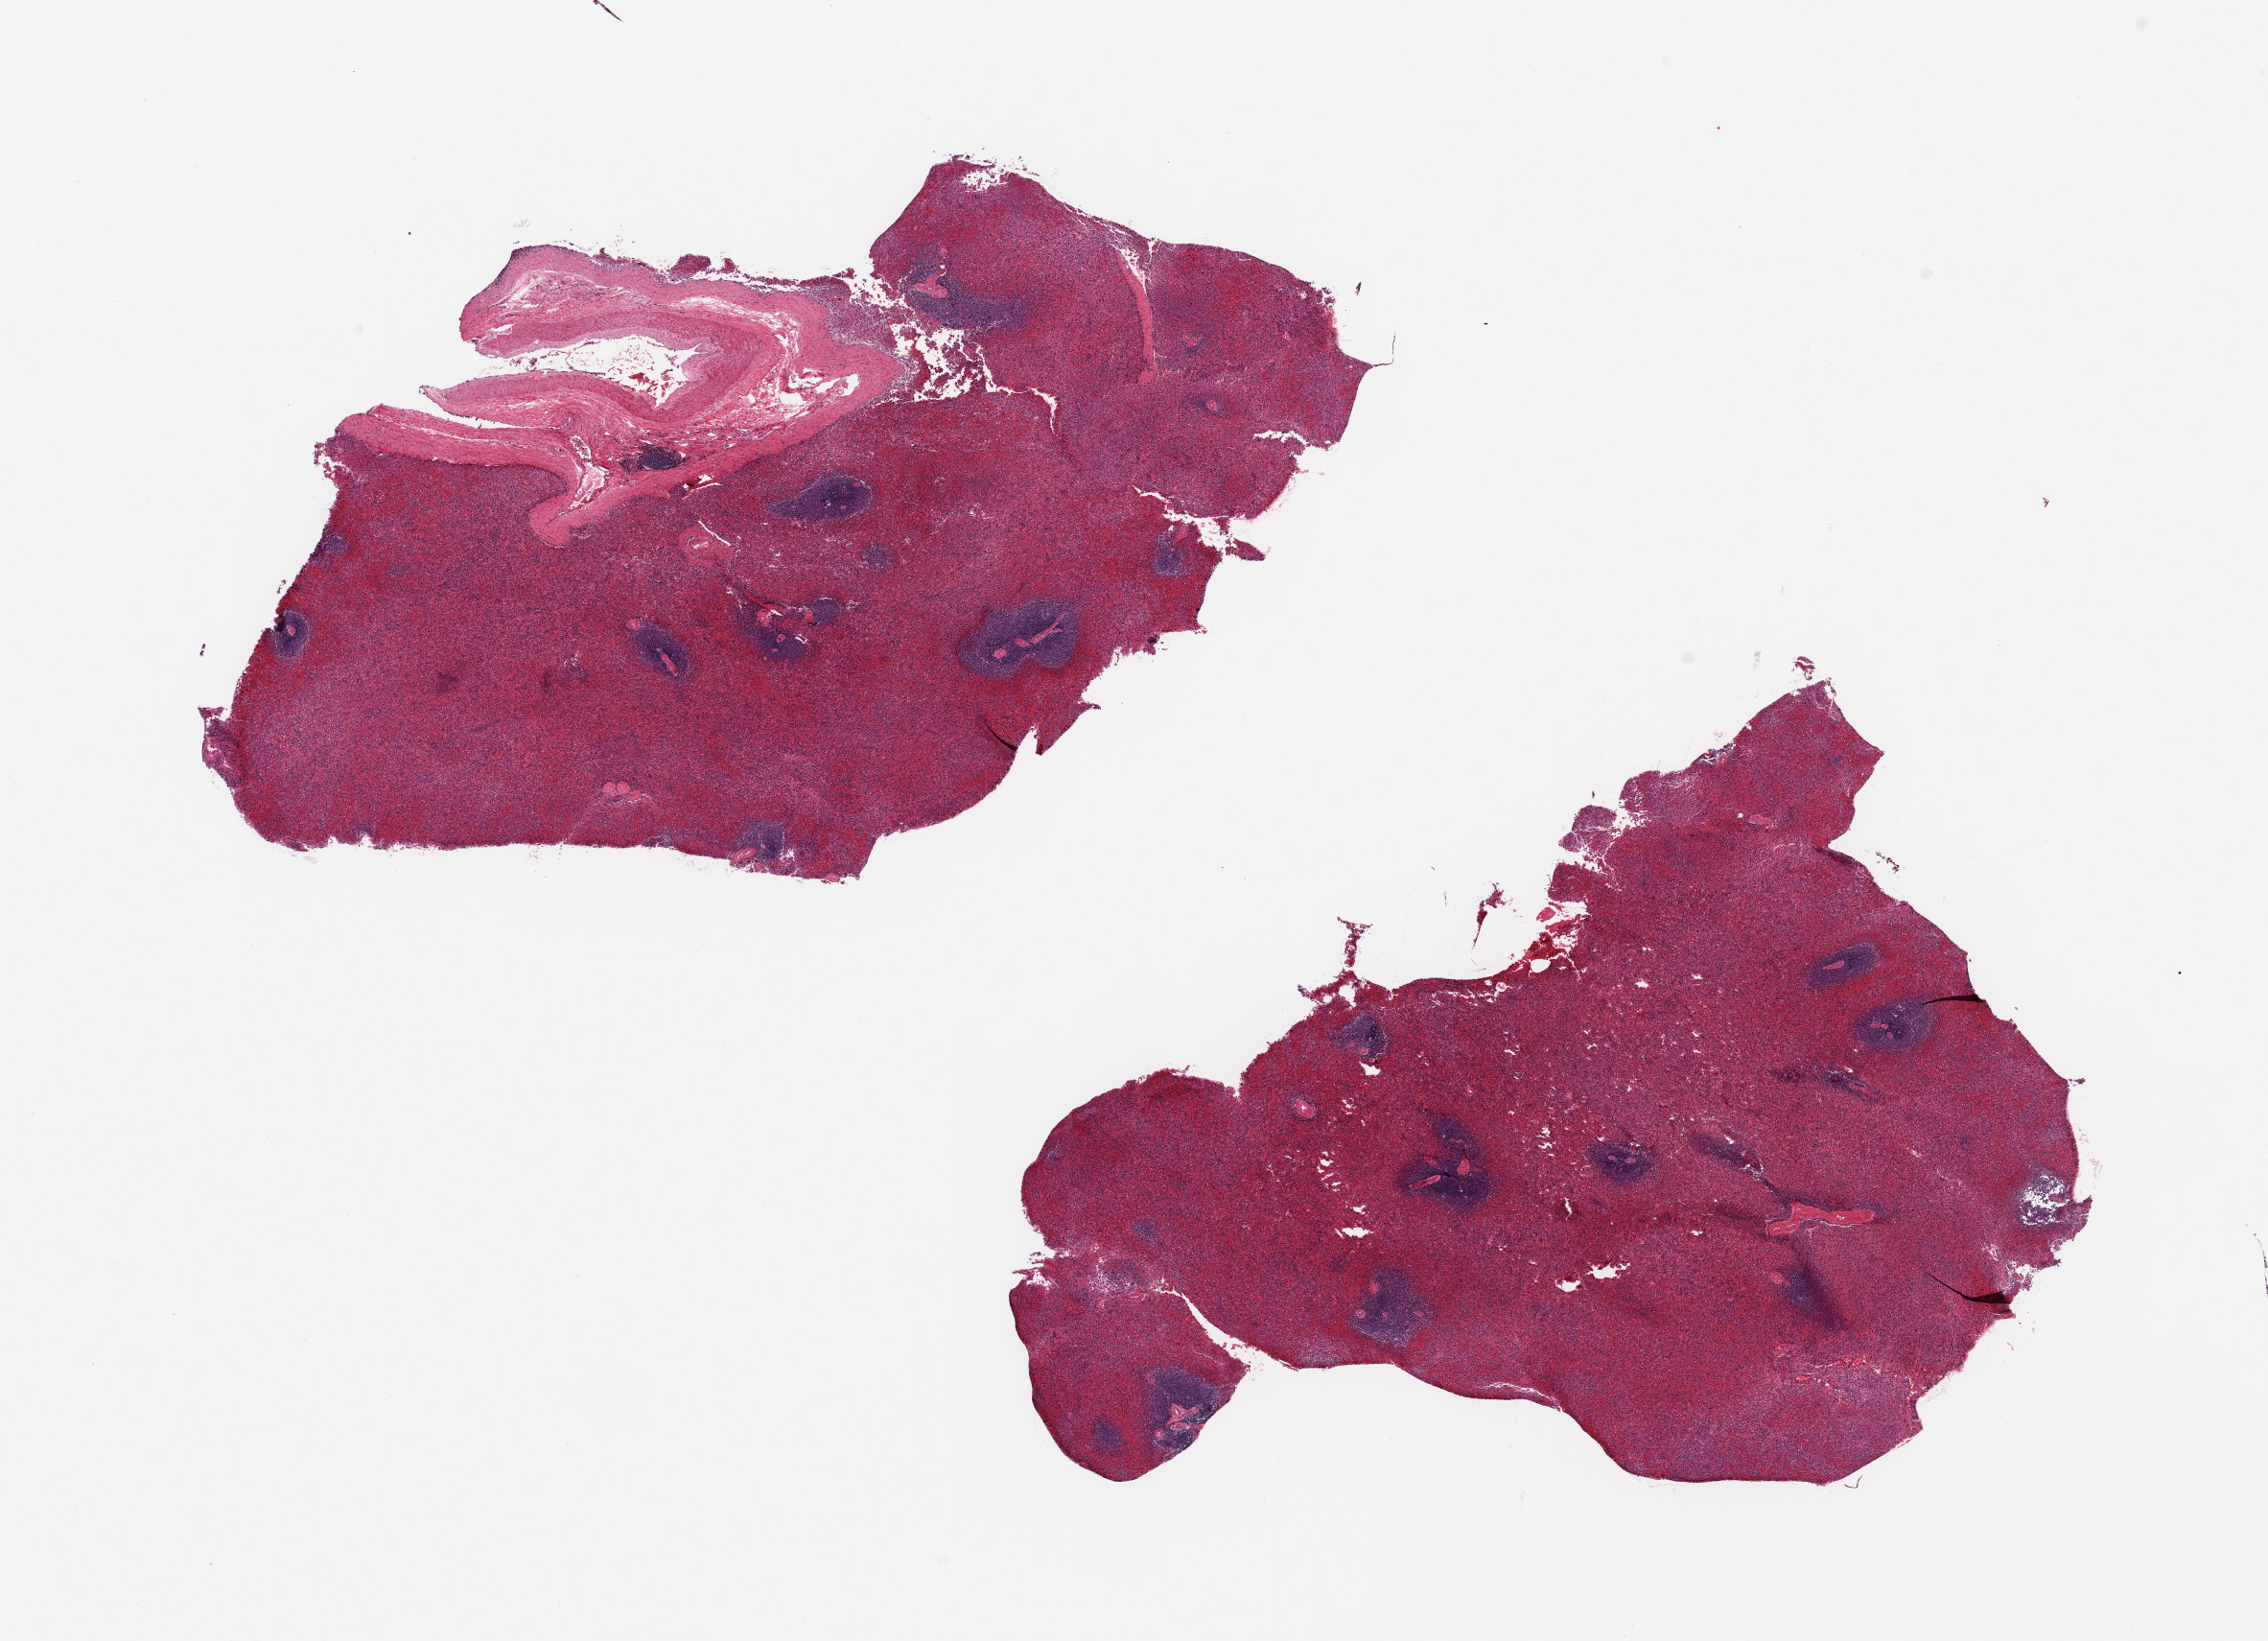
Hematoxylin and eosin (H&E) whole-slide image, shown as a low-resolution overview of the whole scanned area (about 18.7 x 13.5 mm, slide scanned at 20x); PAXgene-fixed paraffin-embedded (PFPE) section; sampled site (target tissue): spleen; tissue donor sample. Male donor.
Pathologist's review note for this sample: 2 pieces, 6x8mm; moderately congested; one piece includes a large perisplenic artery.